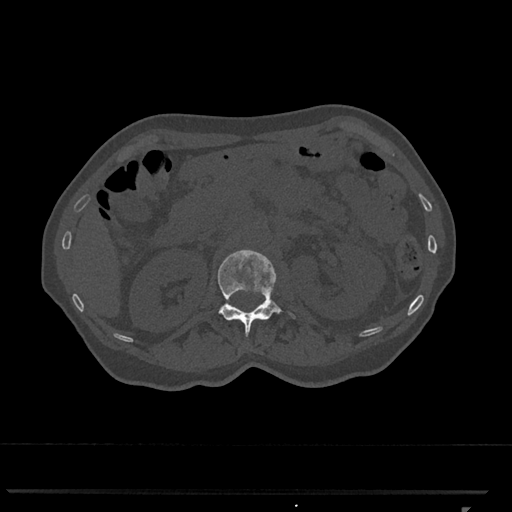
CT including the spine, one axial slice; slice 400 of 793 in the series (ordered by position); reconstruction kernel Br40s/3; bone window (W 1800 / L 400 HU); 0.5 mm slice thickness; 512 × 512 image matrix, field of view 380 × 380 mm. Female patient, age 62 years. From the clinical record (not read from this slice): primary cancer: renal.
Annotated regions visible in this slice (semi-automatic segmentation, software-assisted and operator-edited):
- L1 vertebra: bounding box <217,250,295,338> (left, top, right, bottom; pixels)